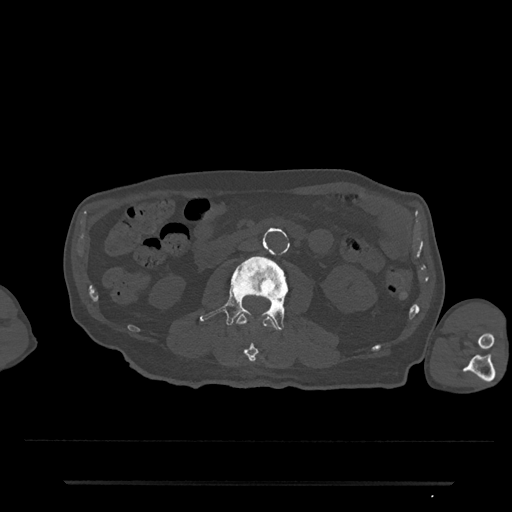
CT including the spine, one axial slice; position 10 of 797 along the scan axis; reconstruction kernel Br40s/3; 120 kVp; bone window (W 1800 / L 400 HU); 0.5 mm slice thickness; 512 × 512 image matrix, field of view 427 × 427 mm. Male patient, age 74 years. From the clinical record (not read from this slice): primary cancer: prostate.
Structures marked on this image (semi-automatic segmentation, software-assisted and operator-edited):
- L2 vertebra: bounding box <235,313,279,362> (left, top, right, bottom; pixels)
- L3 vertebra: <200,254,304,330>